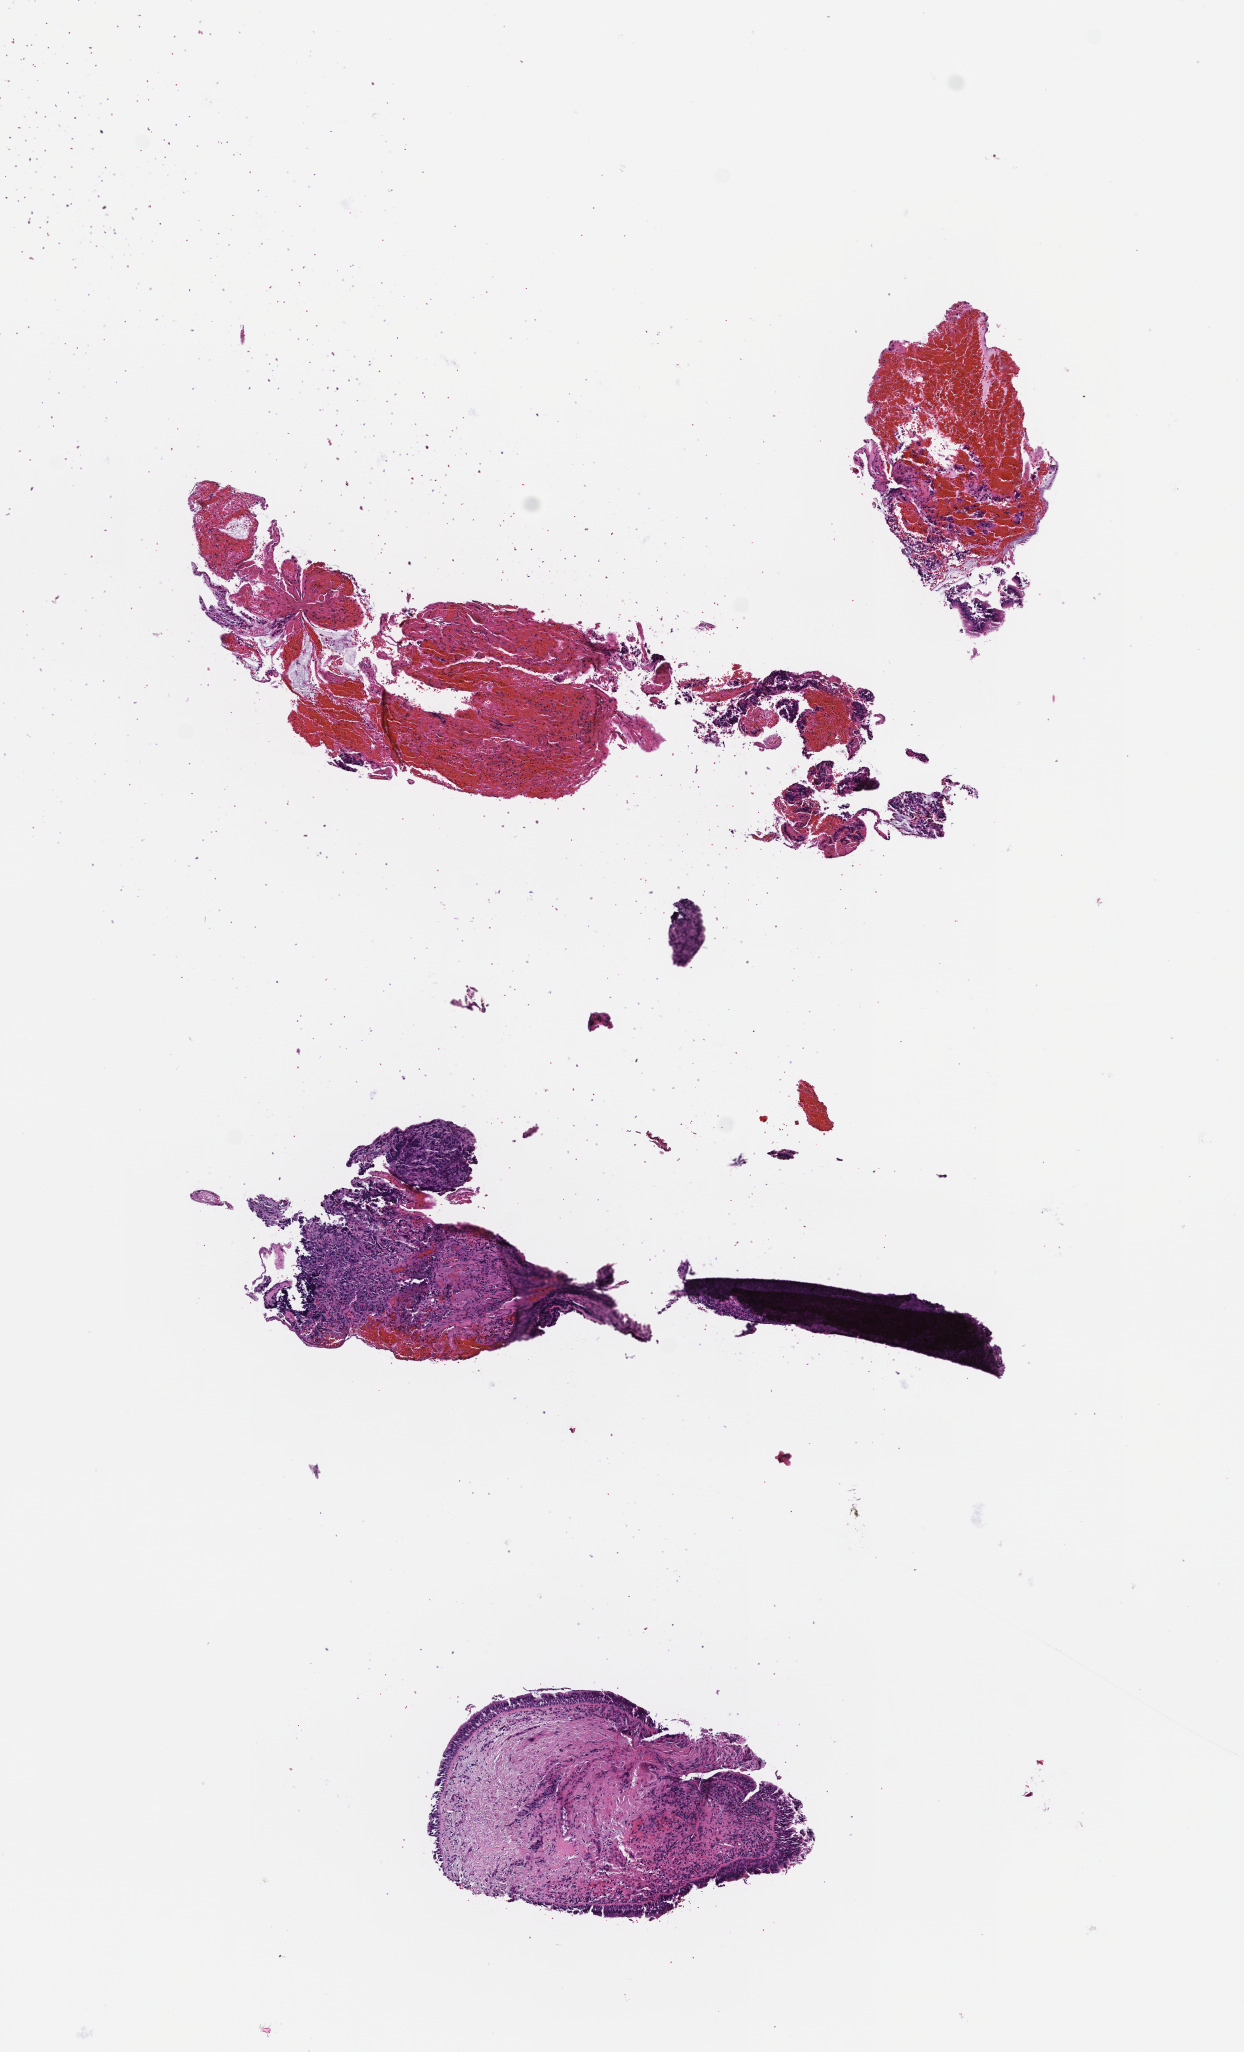
Digitized haematoxylin and eosin-stained section, whole scanned area (about 5.0 x 8.3 mm) shown as a low-resolution overview; FFPE section; site: lung; specimen time point: archival tissue. Patient: male.
- this section: primary tumor
- diagnosis: Non-Small Cell Lung Carcinoma